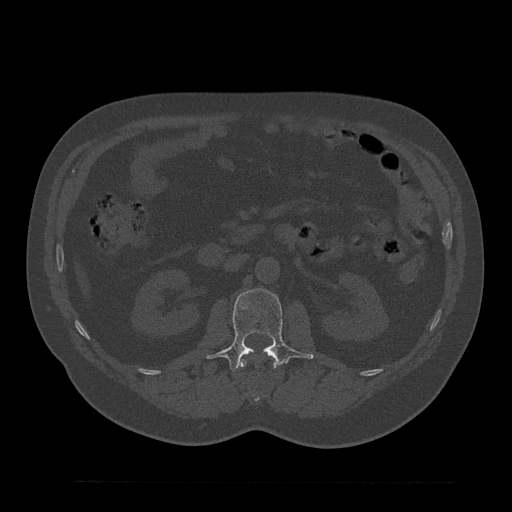
CT including the spine, one axial slice. Position 112 of 797 along the scan axis. 120 kVp. Bone window (W 1800 / L 400 HU). 0.5 mm slice thickness. 512 × 512 image matrix. Patient: male, 61 years. From the clinical record (not read from this slice): primary cancer: prostate.
Annotated regions visible in this slice (semi-automatic segmentation, software-assisted and operator-edited):
- L1 vertebra: bounding box [x1, y1, x2, y2] px = [241, 354, 277, 402]
- L2 vertebra: [208, 288, 313, 371]